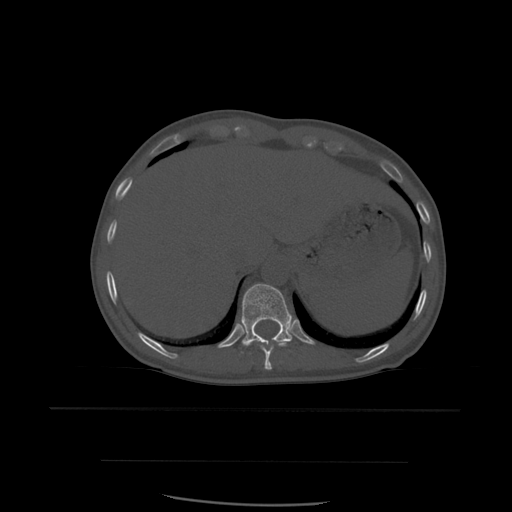
CT including the spine, one axial slice; slice 301 of 574 in the series (ordered by position); bone window (W 1800 / L 400 HU); 1.25 mm slice thickness; 512 × 512 image matrix, field of view 392 × 392 mm. Patient age 48 years. Case-level facts recorded for this patient, not image findings: primary cancer: lung; vertebrae with lytic lesions (as recorded): T11.
Structures marked on this image (semi-automatically segmented with operator editing):
- T10 vertebra: bounding box [x1, y1, x2, y2] px = [260, 341, 289, 370]
- T11 vertebra: [241, 284, 293, 347]